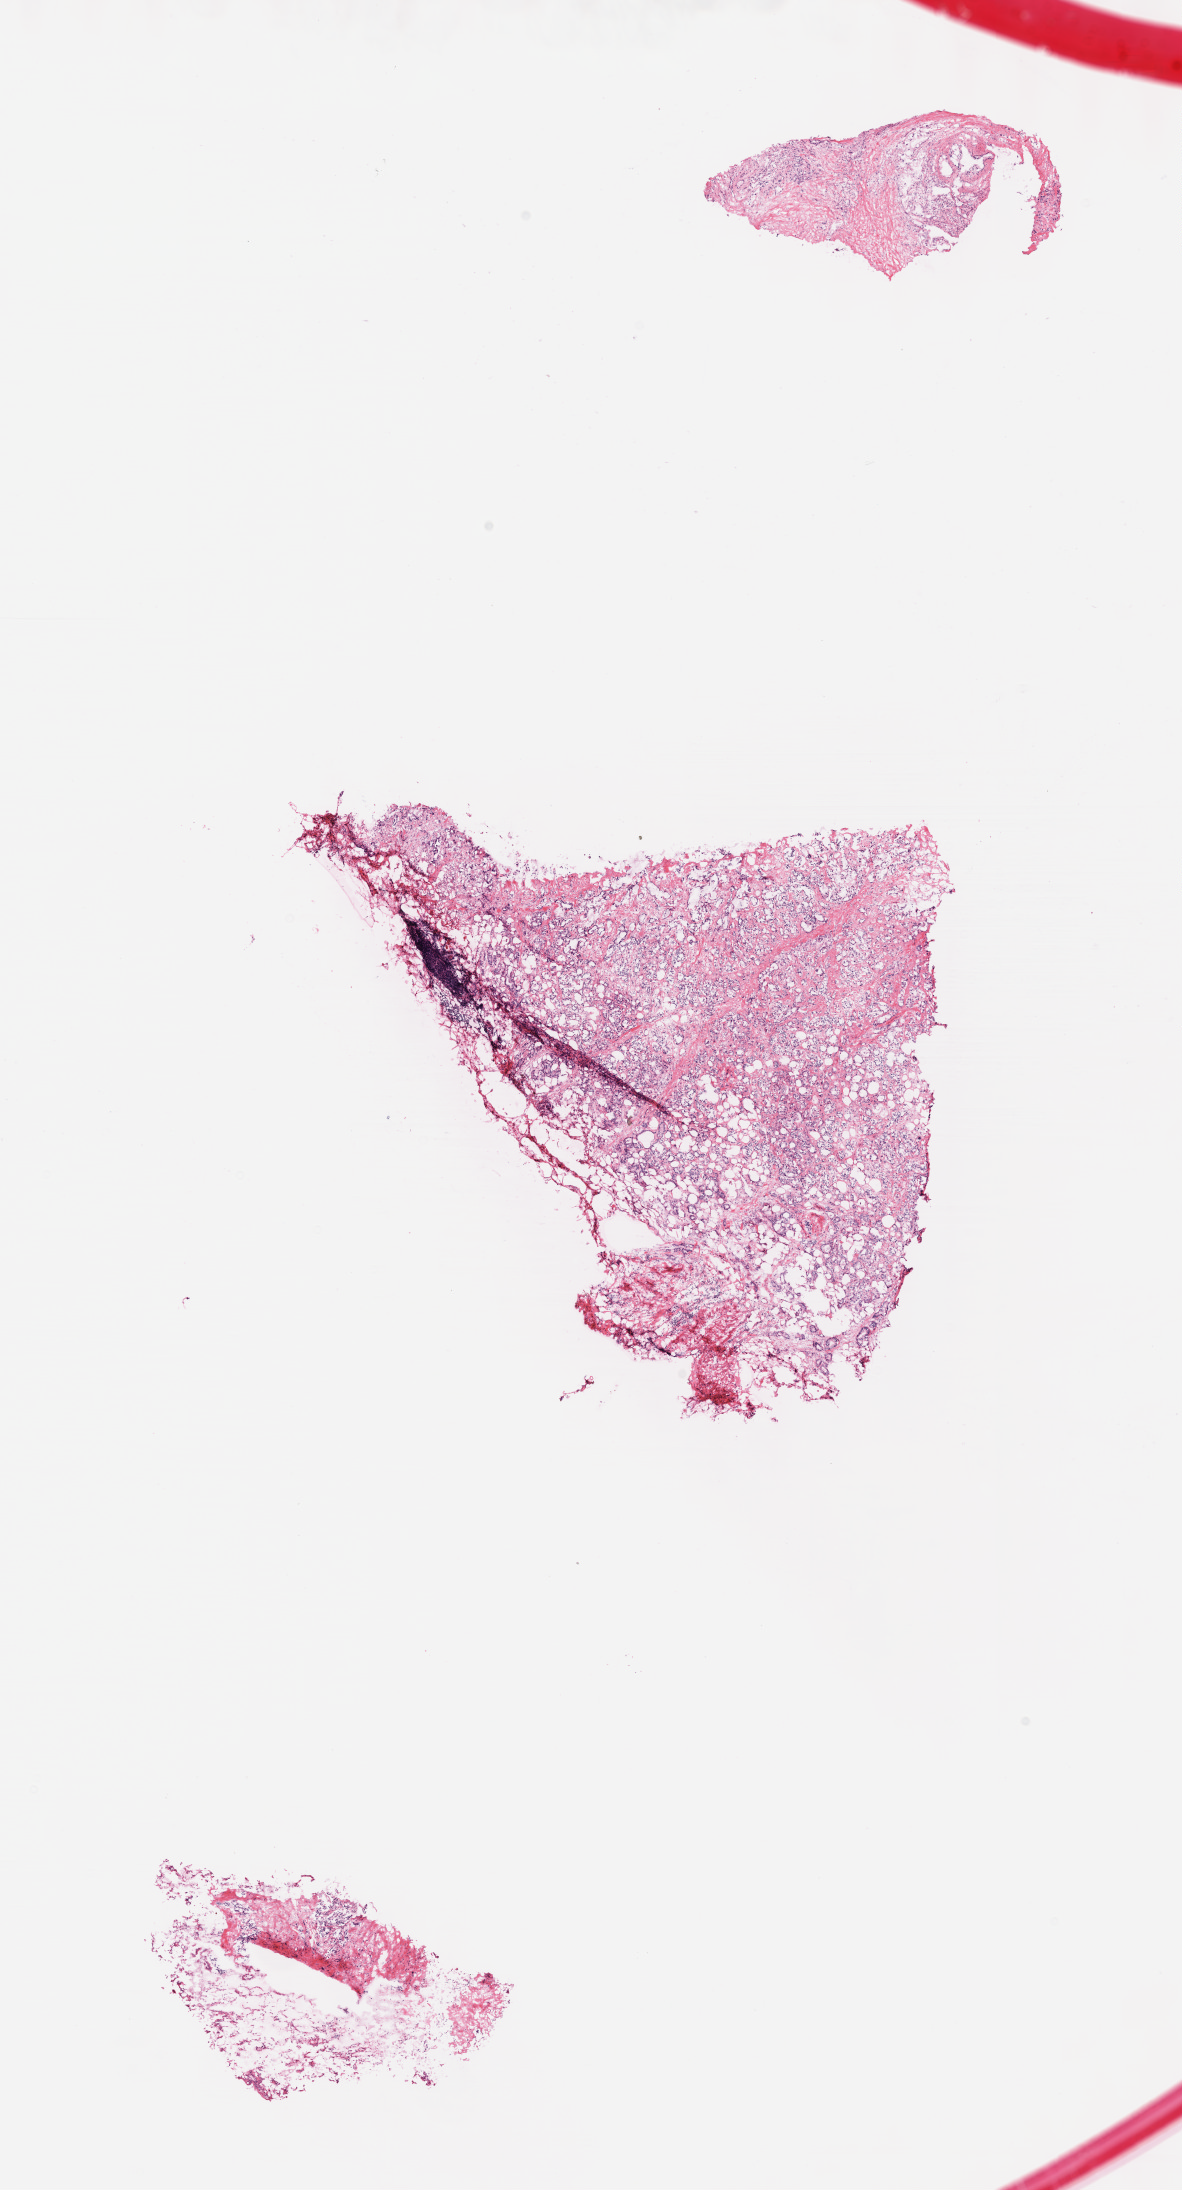
H&E-stained whole-slide image — low-resolution overview of the scanned area, about 9.6 x 17.7 mm (acquisition: 40x scan). Formalin-fixed paraffin-embedded (FFPE) diagnostic section. Pancreas, primary tumour sample. Male, age 54 years at initial diagnosis. Histologic grade: G3 (poorly differentiated).
AJCC pathologic stage: IIB (7th edition). Pathologic diagnosis: Infiltrating duct carcinoma, NOS (head of pancreas).